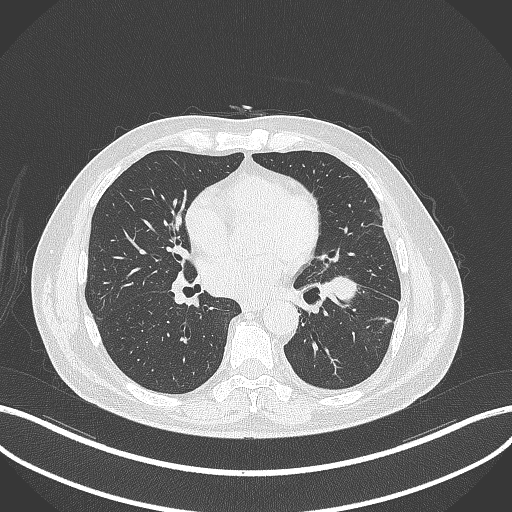
Chest CT, one axial slice; position 169 of 230 along the scan axis; reconstruction kernel B70f; lung window (W 1500 / L -600 HU); 1 mm slice thickness; 512 × 512 image matrix, field of view 400 × 400 mm. Patient: male, 68 years. Case-level facts recorded for this patient, not image findings: clinical TNM (as recorded): T2b N0 M0.
Structures marked on this image (rectangle marked by the reading radiologist):
- lung tumour (recorded histology: squamous cell carcinoma): bounding box [x1, y1, x2, y2] px = [324, 273, 360, 302]